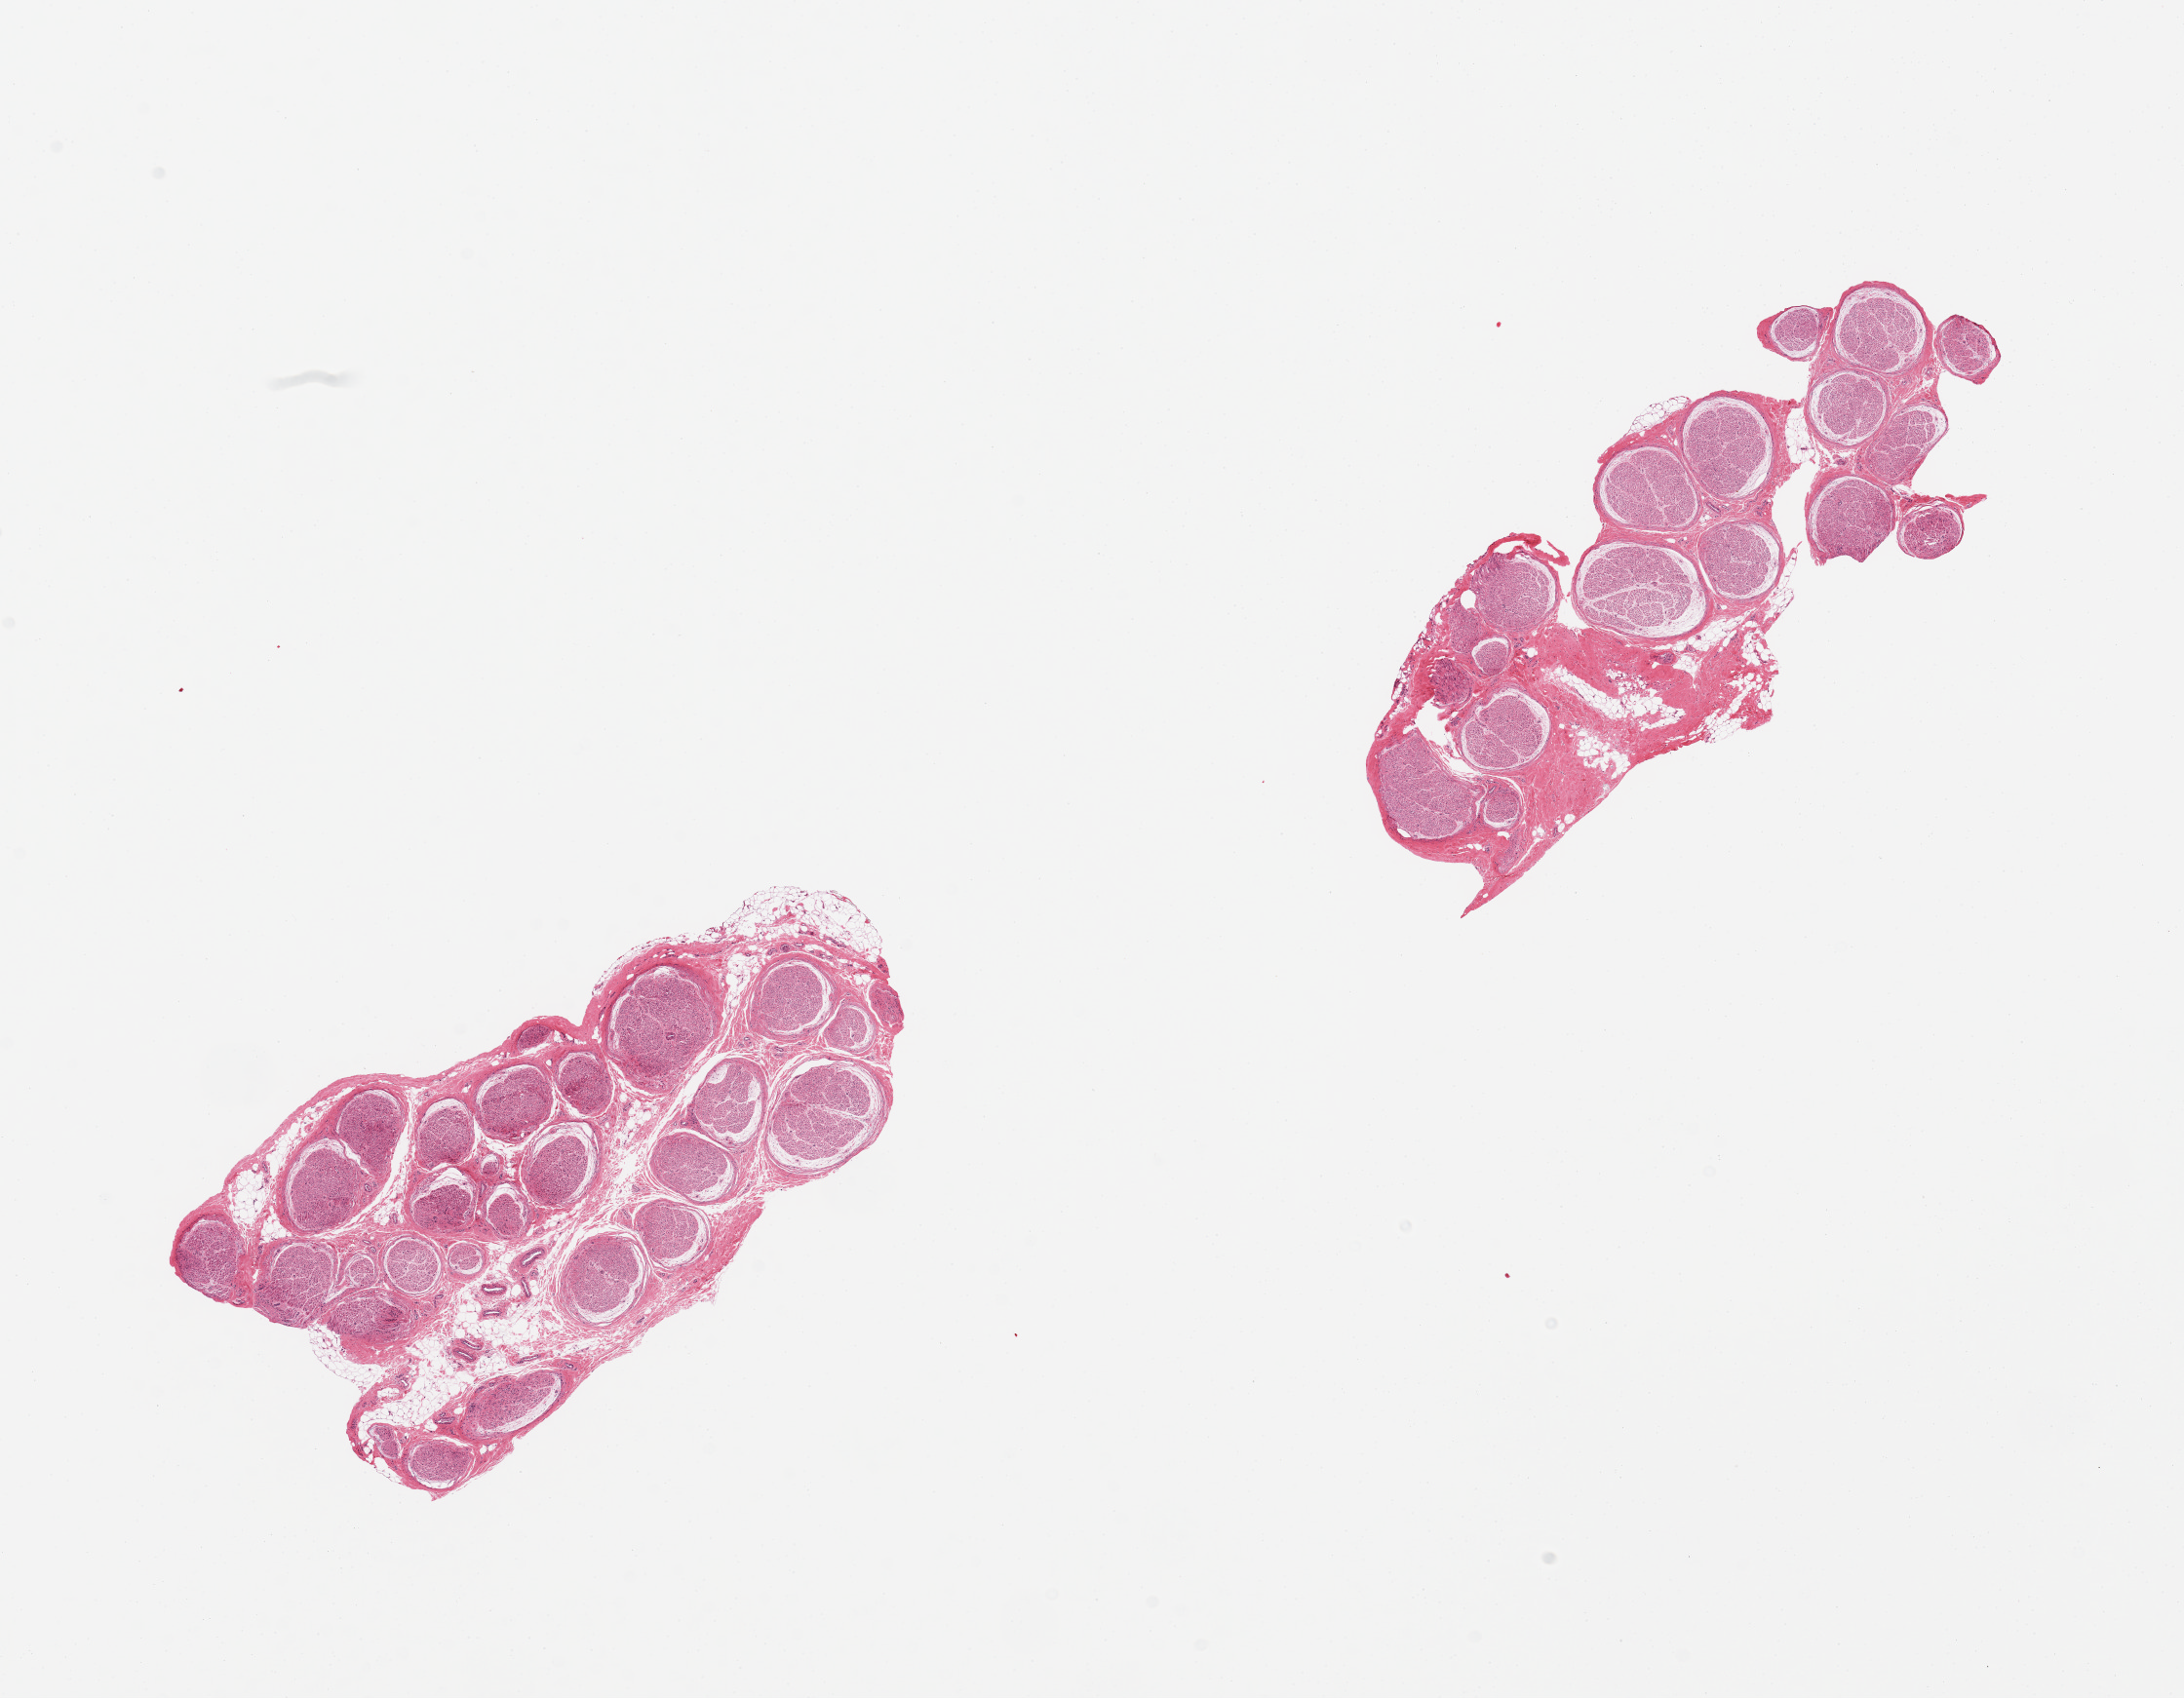
Whole-slide image, hematoxylin and eosin (H&E) stain, brightfield, whole scanned area (about 17.7 x 13.8 mm) shown as a low-resolution overview, PAXgene-fixed, paraffin-embedded tissue, sampled site (target tissue): tibial nerve, tissue donor sample.
* review note (as recorded): 2 pieces clean, minute nubbin of fat